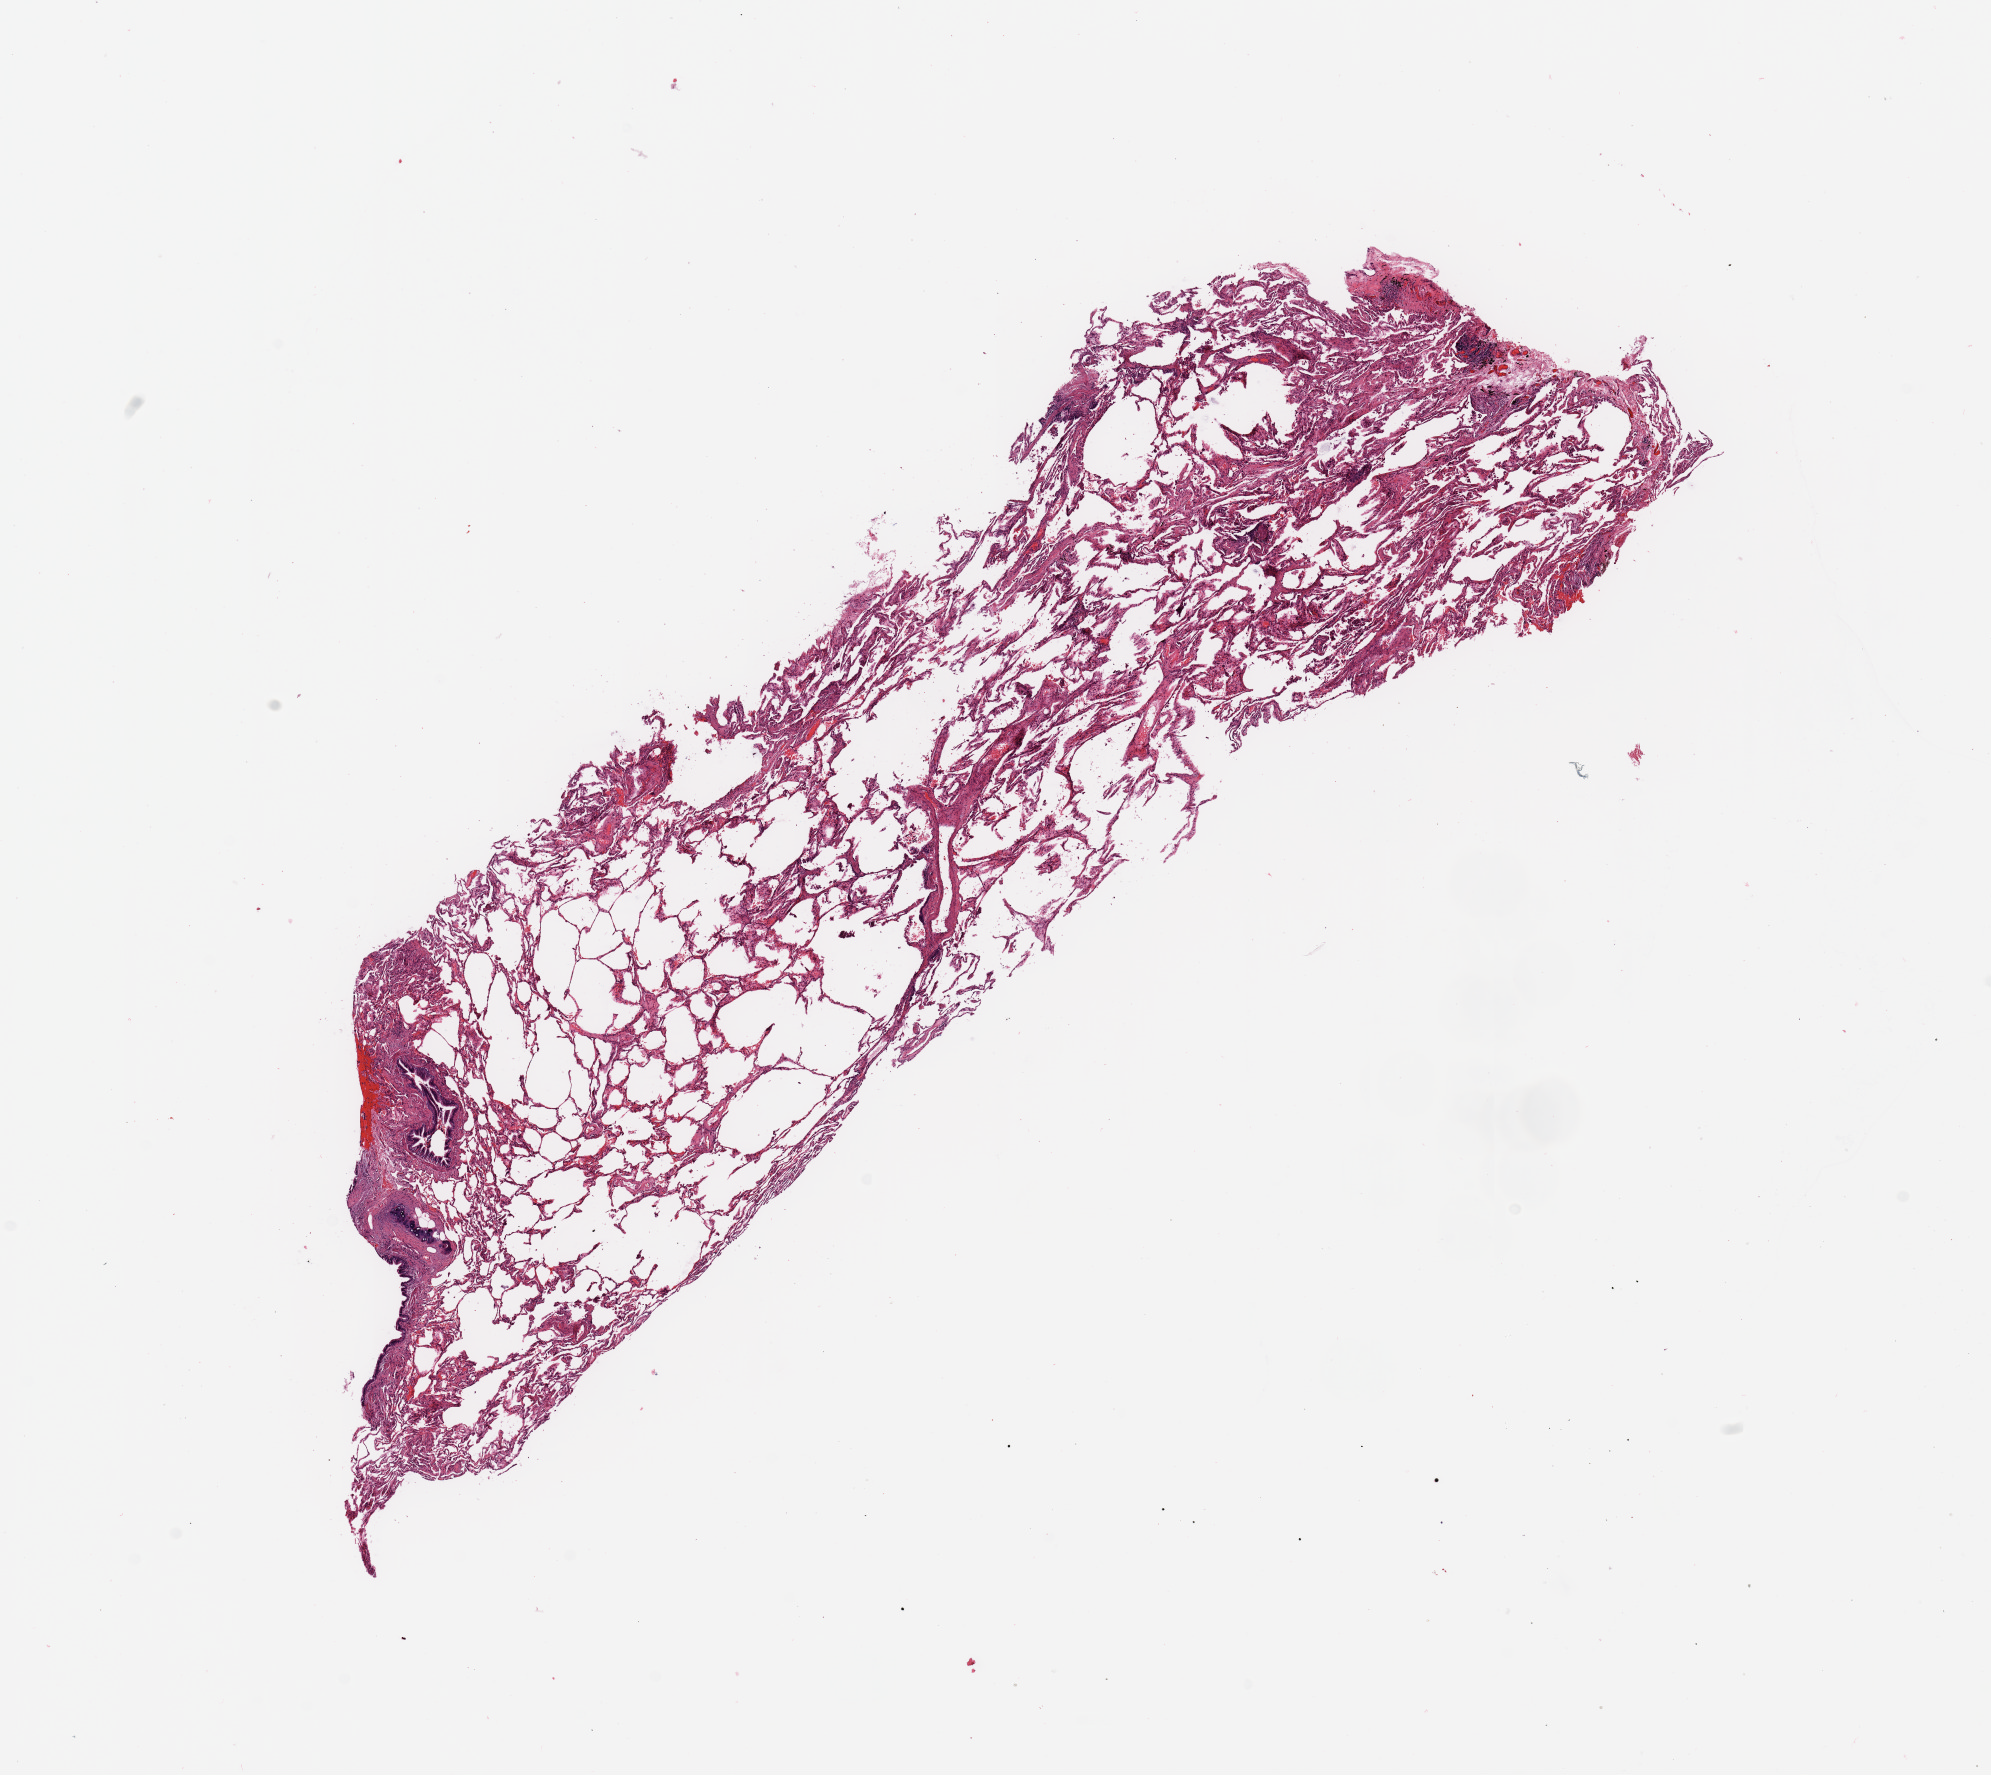
H&E-stained whole-slide image, low-resolution overview of the scanned area, about 15.8 x 14.0 mm. Normal (non-tumour) tissue sample, sampled site: lung. 67-year-old female patient.
This section: normal (non-tumour) tissue from the same patient. Patient diagnosis: Adenocarcinoma, NOS.